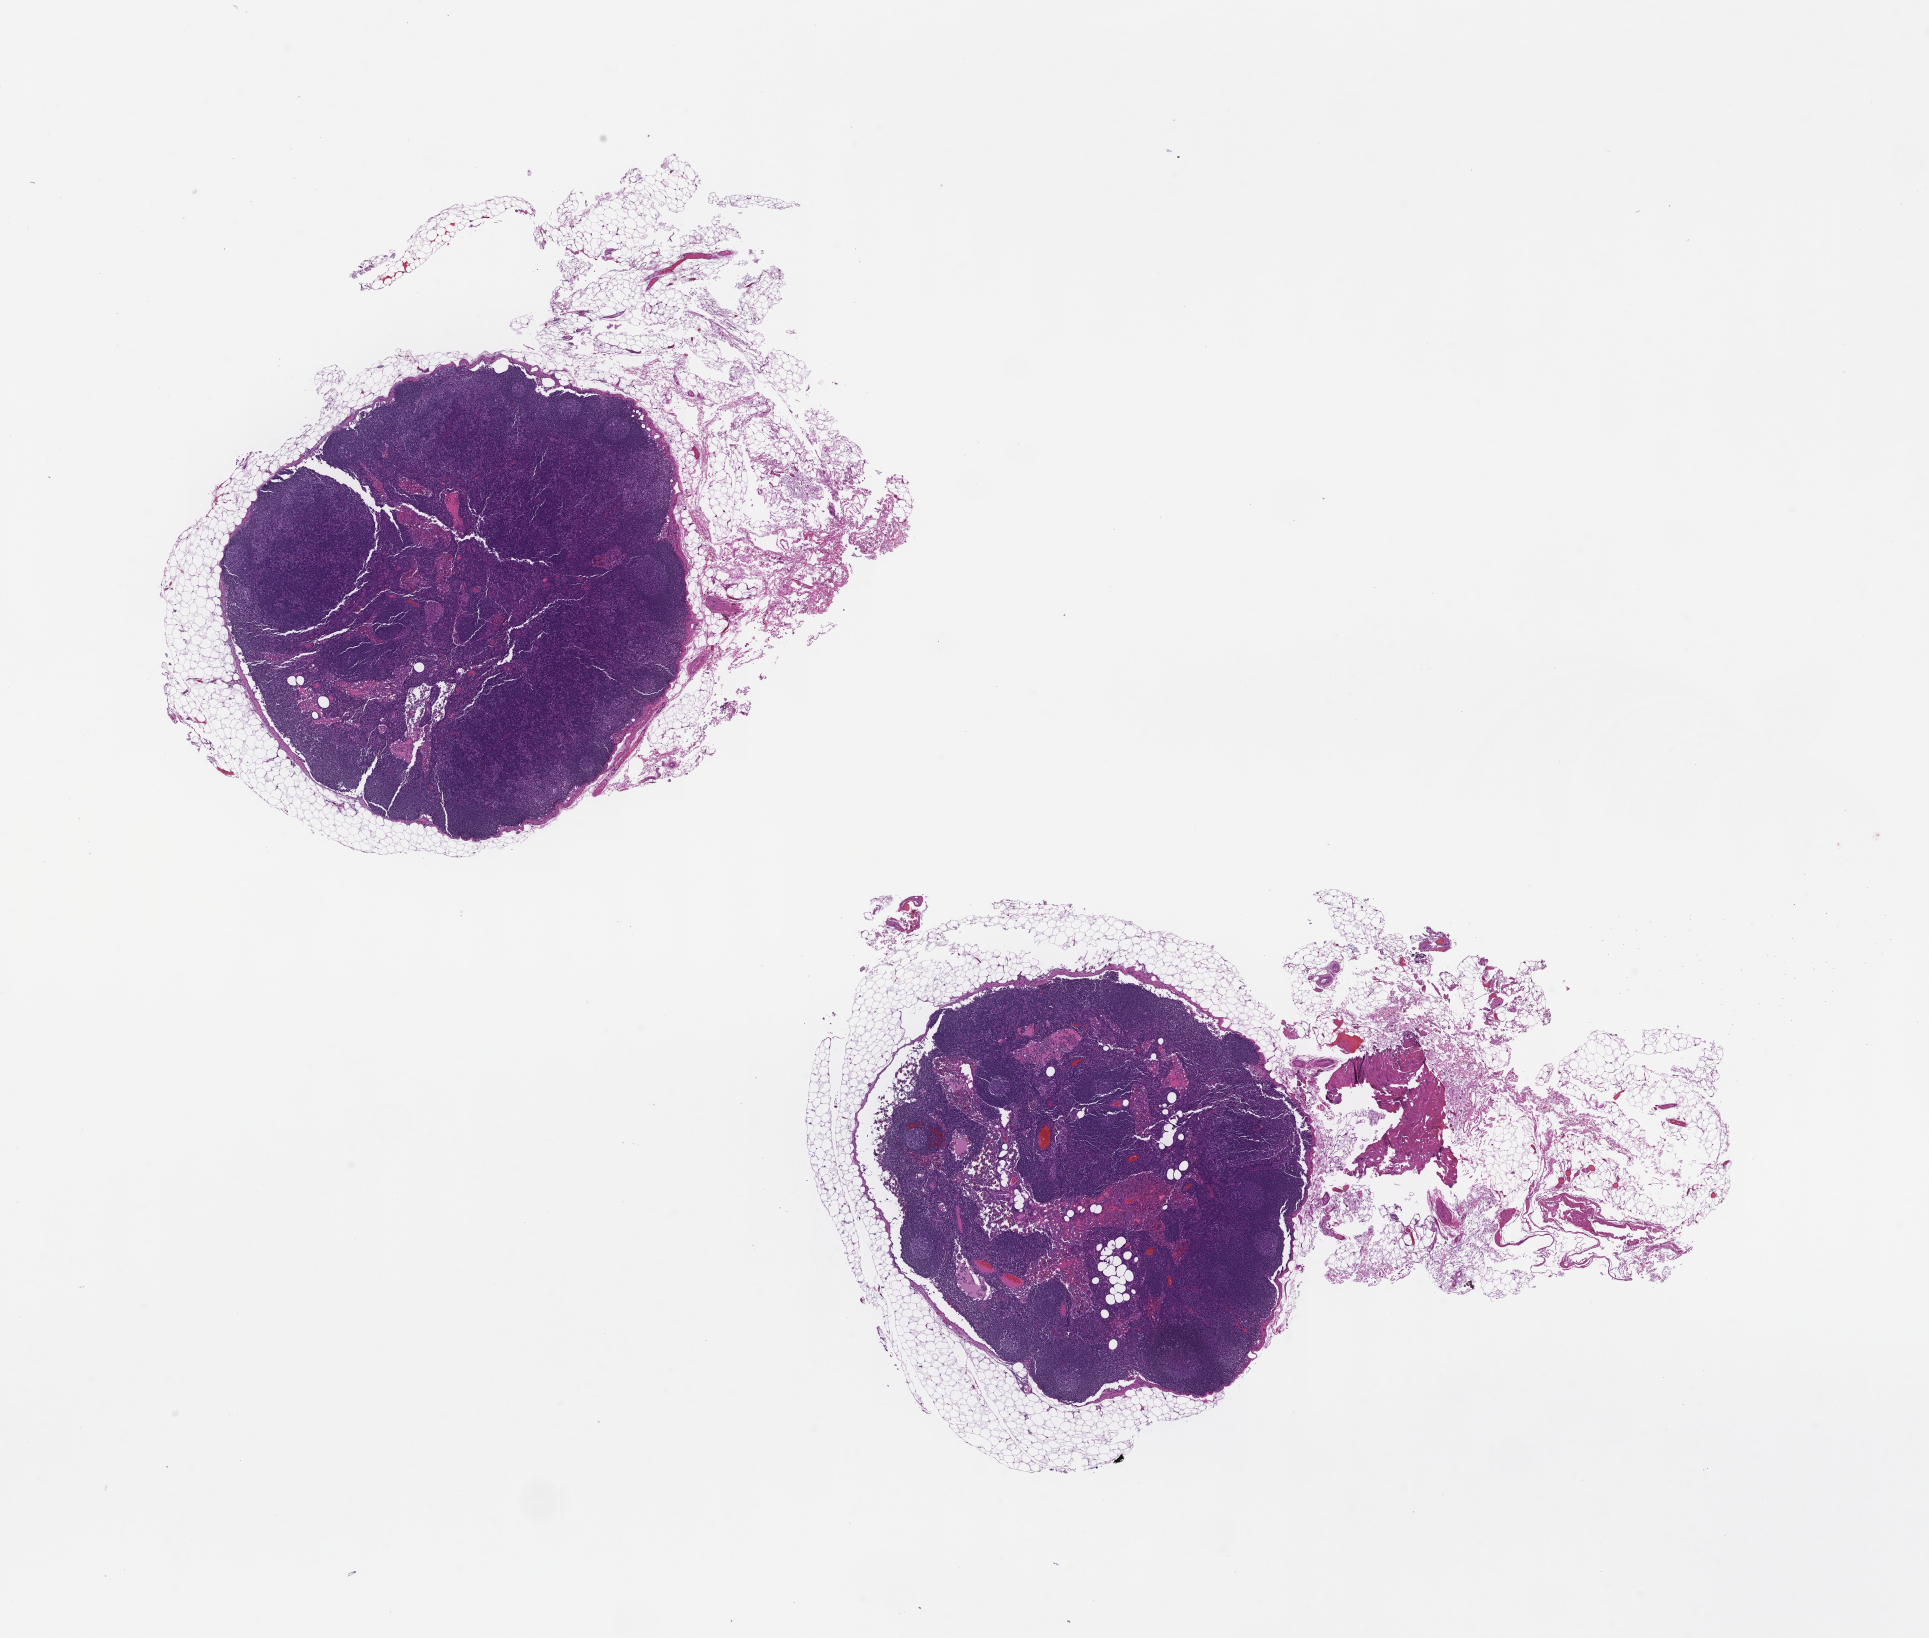
Whole-slide image, hematoxylin and eosin (H&E) stain, whole scanned area (about 15.6 x 13.2 mm) shown as a low-resolution overview. Formalin-fixed paraffin-embedded section. Site: skin. Specimen time point: archival tissue. Patient: female.
* this section: primary tumour tissue
* diagnosis: Melanoma